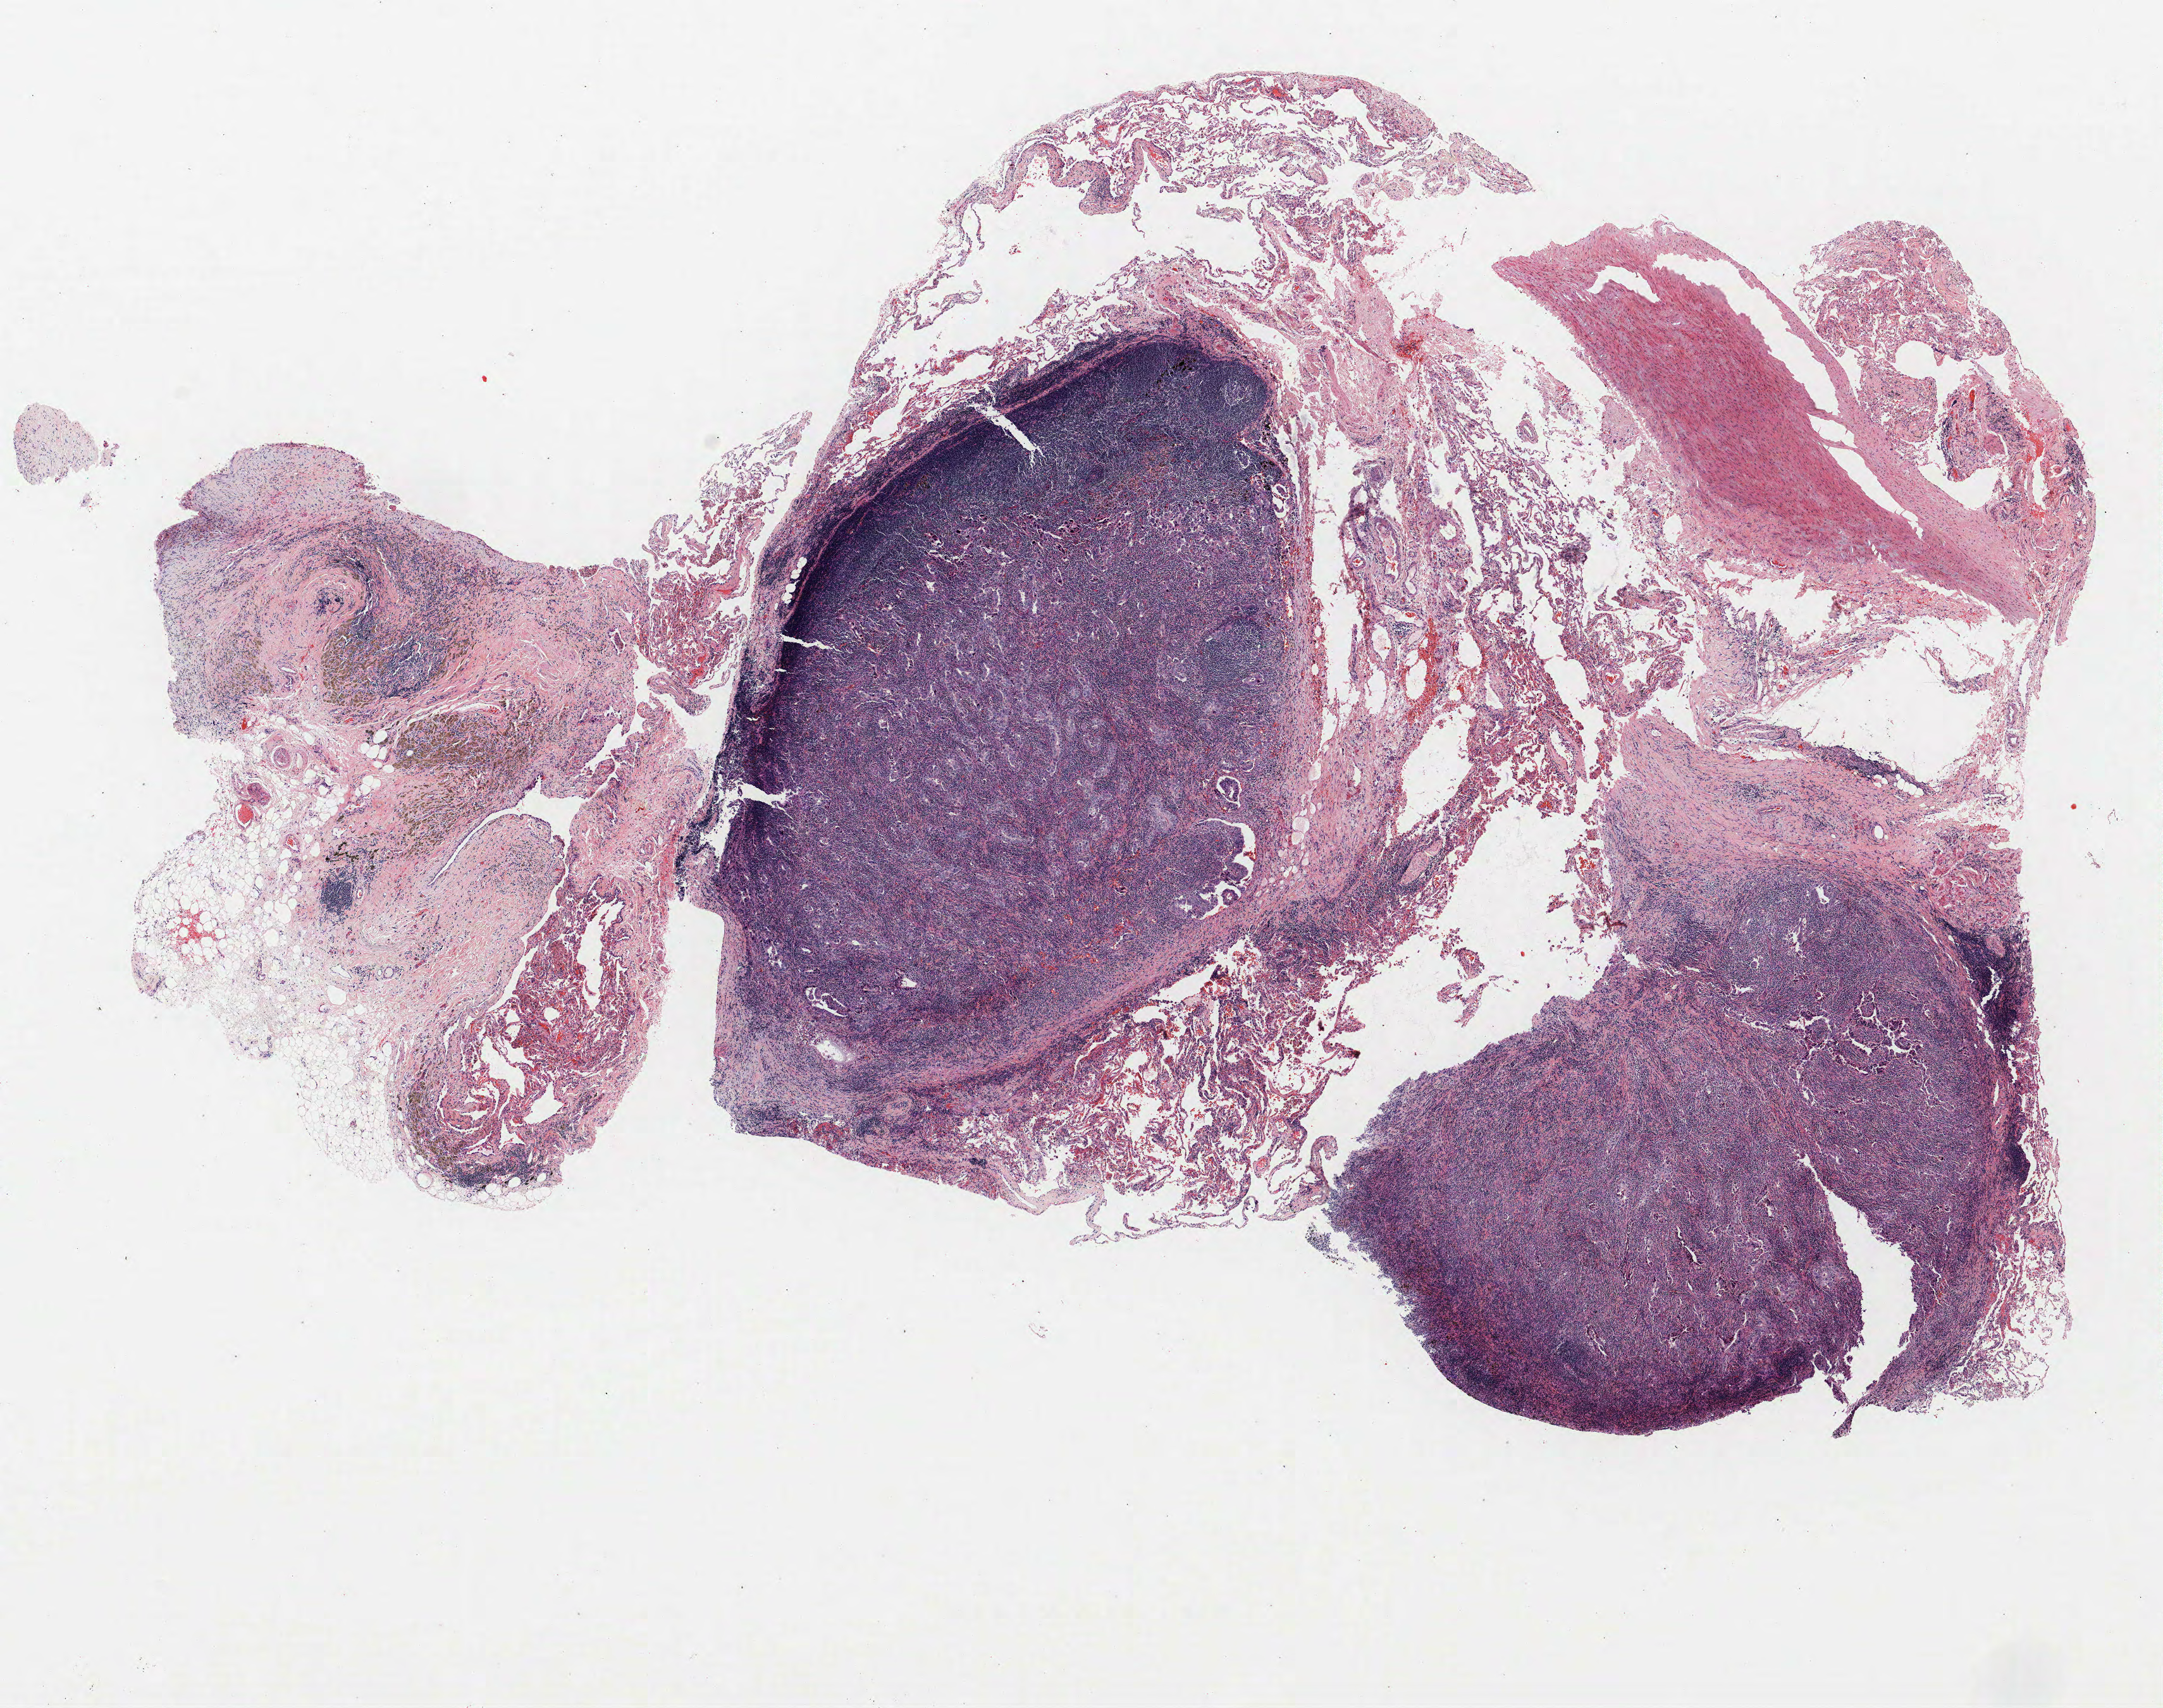
H&E whole-slide image, low-resolution overview of the scanned area, about 13.7 x 10.8 mm (slide scanned at 40x), FFPE section, lung tissue. Male patient, aged 63 at enrolment. Current smoker at enrolment. Grade: moderately differentiated (G2).
- stage (AJCC 6th edition): IIIB
- participant's lung-cancer diagnosis: Adenocarcinoma, NOS
- primary tumour location (clinical record): right upper lobe
- tumour size (pathology): 17 mm